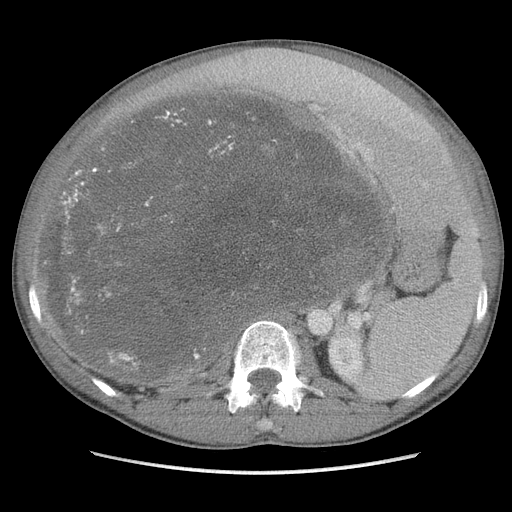
Contrast-enhanced abdominal CT, one axial slice. Position 65 of 115 along the scan axis. Soft-tissue window (W 400 / L 40 HU). 5 mm slice thickness. 512 × 512 image matrix, field of view 360 × 360 mm. Male patient. Case-level facts recorded for this patient, not image findings: diagnosis: adrenocortical carcinoma; tumour side: right adrenal; Ki-67 index: 13 %; stage (as recorded): 3.
Outlined on this slice (semi-automatic segmentation, software-assisted and operator-edited):
- mass: box from (x=52, y=89) to (x=388, y=380) px